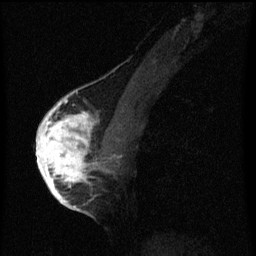
Breast MRI (dynamic contrast-enhanced), one sagittal slice. Position 33 of 60 along the scan axis. Dynamic contrast-enhanced series, image 2 of 3 at this slice position (ordered by acquisition). 1.5 T. TE 4.2 ms, TR 8 ms. 256 × 256 image matrix, field of view 180 × 180 mm. Patient: female, 56 years.
Annotated regions visible in this slice (semi-automatically segmented with operator editing):
- analysis volume of interest (the breast-tissue region the enhancement analysis was run in; not a lesion): bounding box <42,110,103,193> (left, top, right, bottom; pixels)
- tumour enhancement mask (voxels above the 70 % enhancement threshold inside the analysis volume of interest): <42,110,95,193>